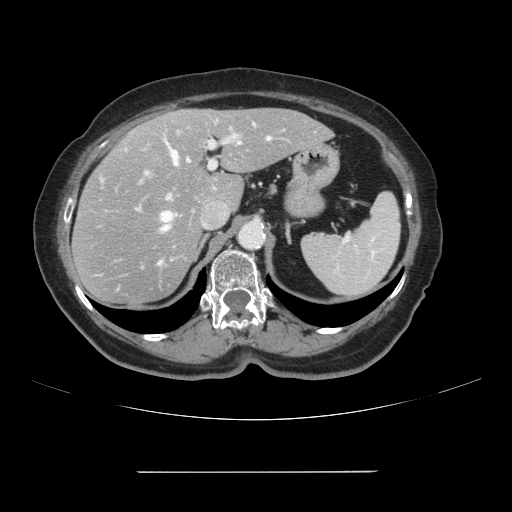
Contrast-enhanced abdominal CT, one axial slice; position 68 of 111 along the scan axis; intravenous contrast given; soft-tissue window (W 400 / L 40 HU); 512 × 512 image matrix, field of view 400 × 400 mm. Female patient, age 74 years. From the clinical record (not read from this slice): diagnosis: colorectal cancer liver metastases, imaged before liver resection; multiple liver metastases: yes; largest metastasis: 1.1 cm; chemotherapy before resection: yes.
Annotated regions visible in this slice (manually delineated by an expert):
- hepatic veins: box from (x=116, y=137) to (x=271, y=291) px
- liver: (x=74, y=109)–(x=331, y=306)
- planned liver remnant (the part of the liver to remain after resection): (x=150, y=109)–(x=331, y=208)
- portal vein (with intrahepatic branches): (x=144, y=130)–(x=285, y=201)